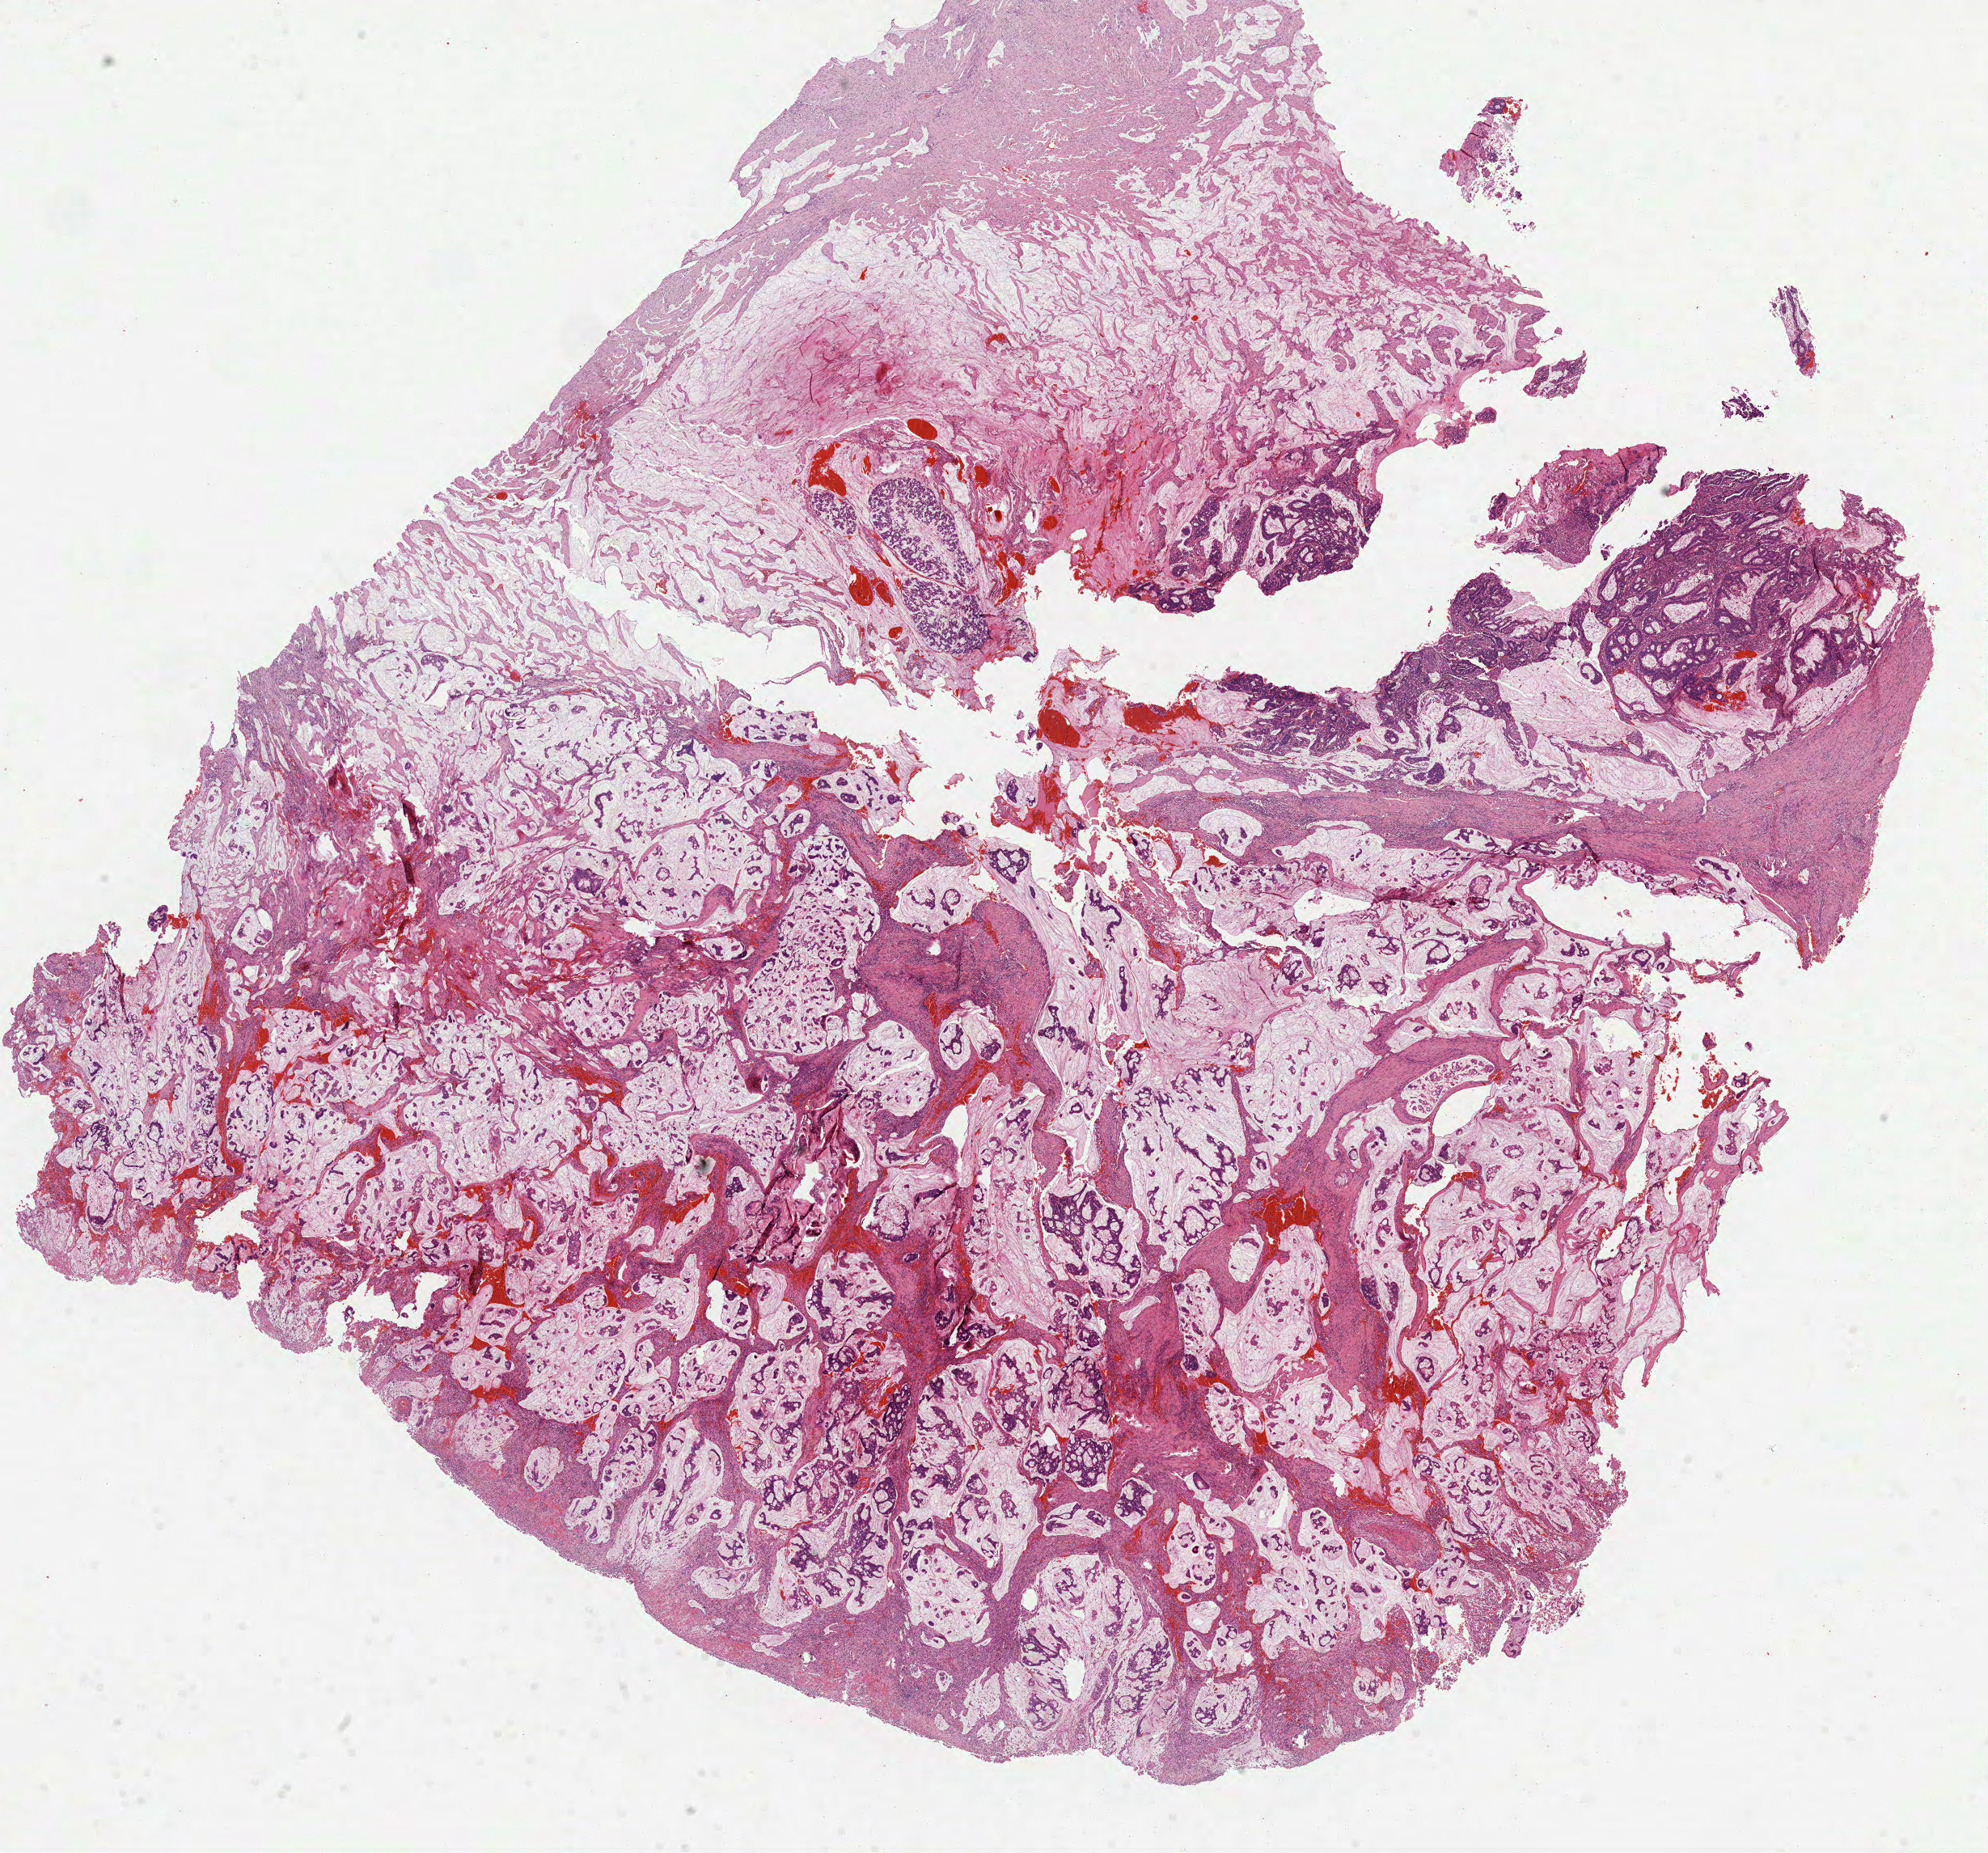
H&E-stained whole-slide image, a low-resolution overview of the entire scanned area, about 19.8 x 18.5 mm; FFPE section; primary tumour sample from the rectum. Male, age 60 years at initial diagnosis.
Histologic diagnosis: Mucinous adenocarcinoma. AJCC pathologic stage: IIA (7th edition).